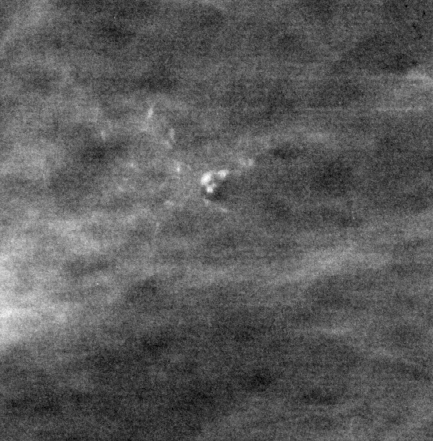
Cropped region of a digitized screen-film mammogram centred on a radiologist-marked abnormality, right breast, MLO view, BI-RADS breast density category 1 (scale 1–4).
Calcifications, morphology amorphous, distribution clustered; BI-RADS assessment category 4; pathology (as recorded): malignant.